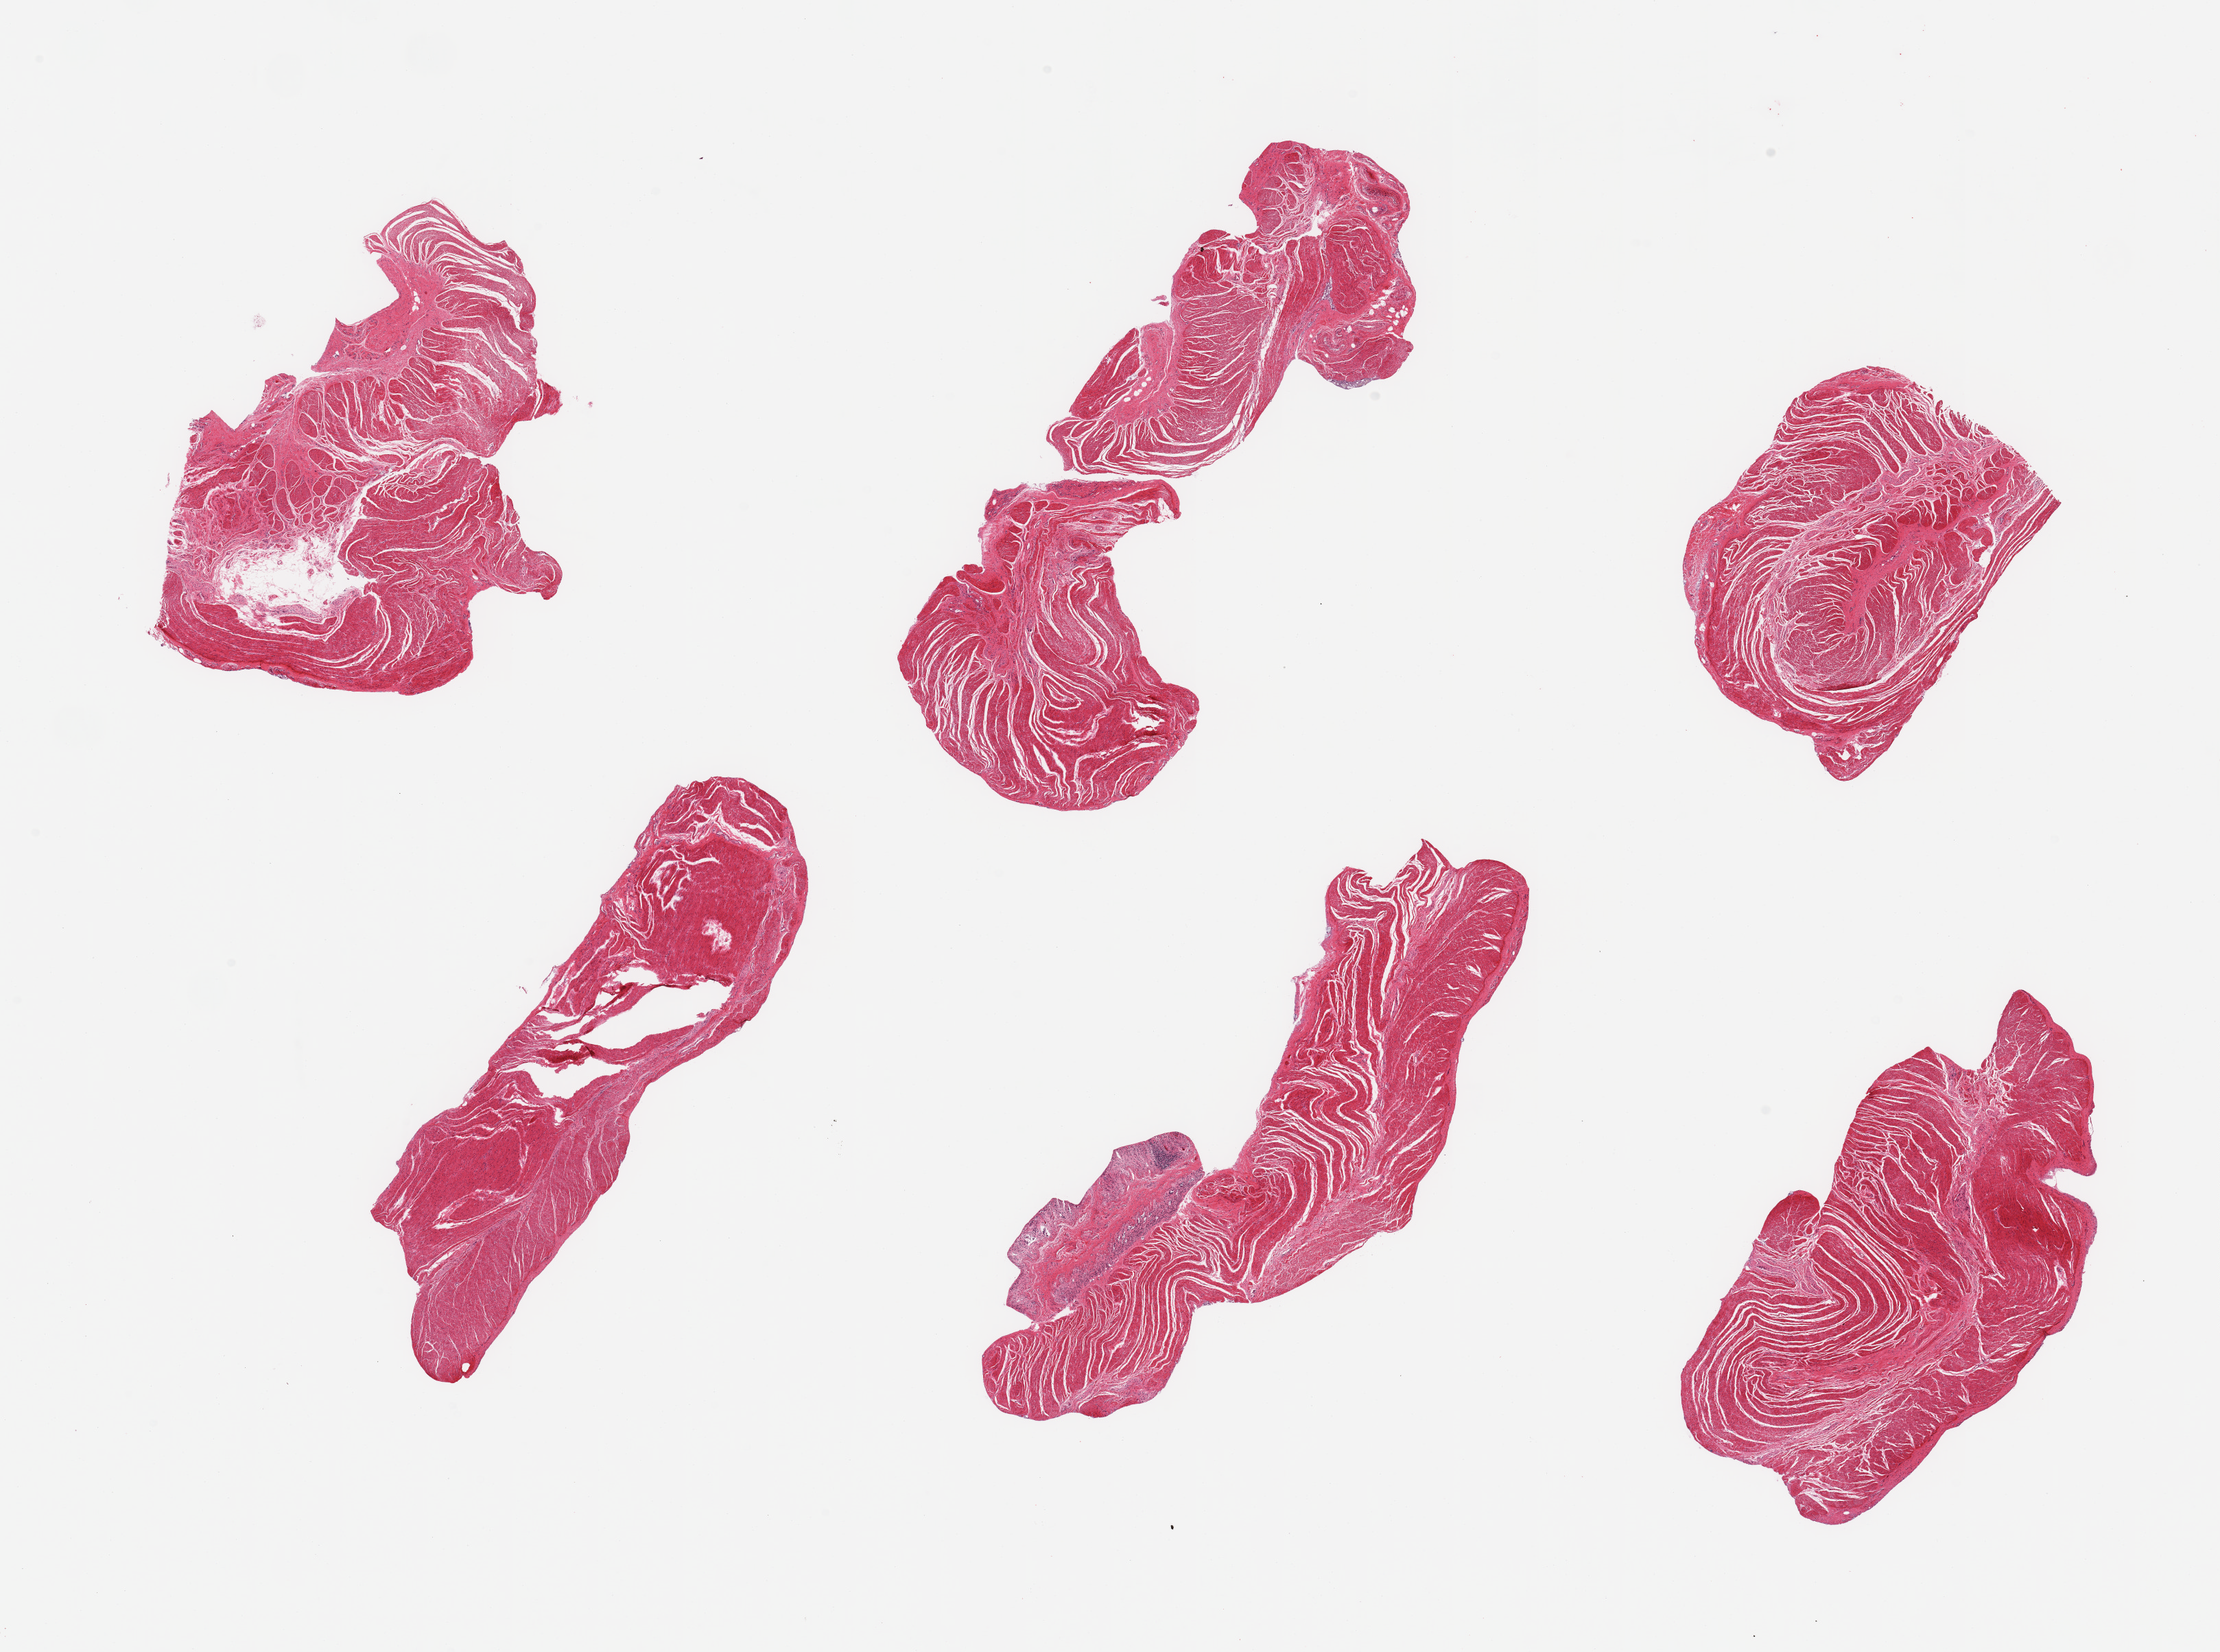
Digitized hematoxylin and eosin (H&E)-stained section — low-resolution overview of the scanned area, about 25.6 x 19.0 mm; PAXgene-fixed, paraffin-embedded tissue; section of sigmoid colon (target tissue); tissue donor sample.
Reviewer comment on this tissue sample: 6 pieces; predominantly target muscularis with focus of autolyzed mucosa.